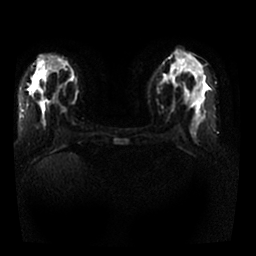
Breast MRI, one axial slice. Slice 12 of 25 in the series (ordered by position). Diffusion-weighted series; image 2 of 4 stored at this slice position (different b-values; order by instance number). 1.5 T. 256 × 256 image matrix, field of view 330 × 330 mm. Female patient.
Structures marked on this image (manually delineated by an expert):
- tumour on diffusion-weighted imaging: bounding box [x1, y1, x2, y2] px = [30, 88, 44, 107]